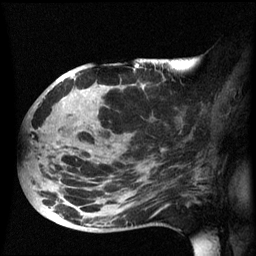
Breast MRI (dynamic contrast-enhanced), one sagittal slice; dynamic contrast-enhanced series, image 2 of 3 at this slice position (ordered by acquisition); 1.5 T; TE 4.2 ms, TR 8.4 ms; 2.5 mm slice thickness; 256 × 256 image matrix. Patient: female, 49 years.
Outlined on this slice (semi-automatically segmented with operator editing):
- analysis volume of interest (the breast-tissue region the enhancement analysis was run in; not a lesion): bounding box (x1, y1, x2, y2) in pixels: (24, 72, 184, 233)
- tumour enhancement mask (voxels above the 70 % enhancement threshold inside the analysis volume of interest): (72, 76, 90, 227)